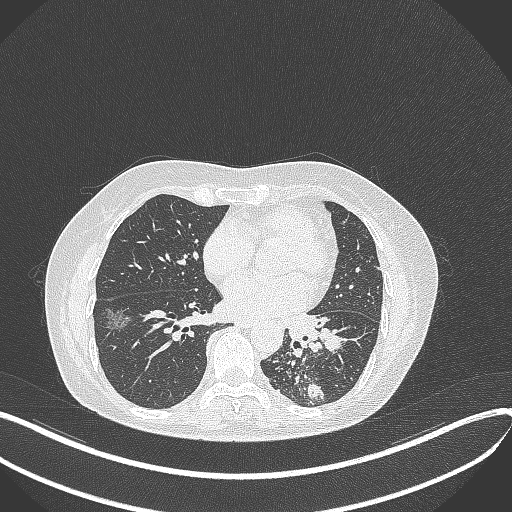
Chest CT, one axial slice. Position 173 of 429 along the scan axis. 100 kVp. Lung window (W 1500 / L -600 HU). 512 × 512 image matrix, field of view 400 × 400 mm. Female patient, age 63 years. Case-level facts recorded for this patient, not image findings: clinical TNM (as recorded): T1b N0 M0.
Structures marked on this image (rectangle marked by the reading radiologist):
- lung tumour (recorded histology: adenocarcinoma): bounding box <282,303,349,361> (left, top, right, bottom; pixels)